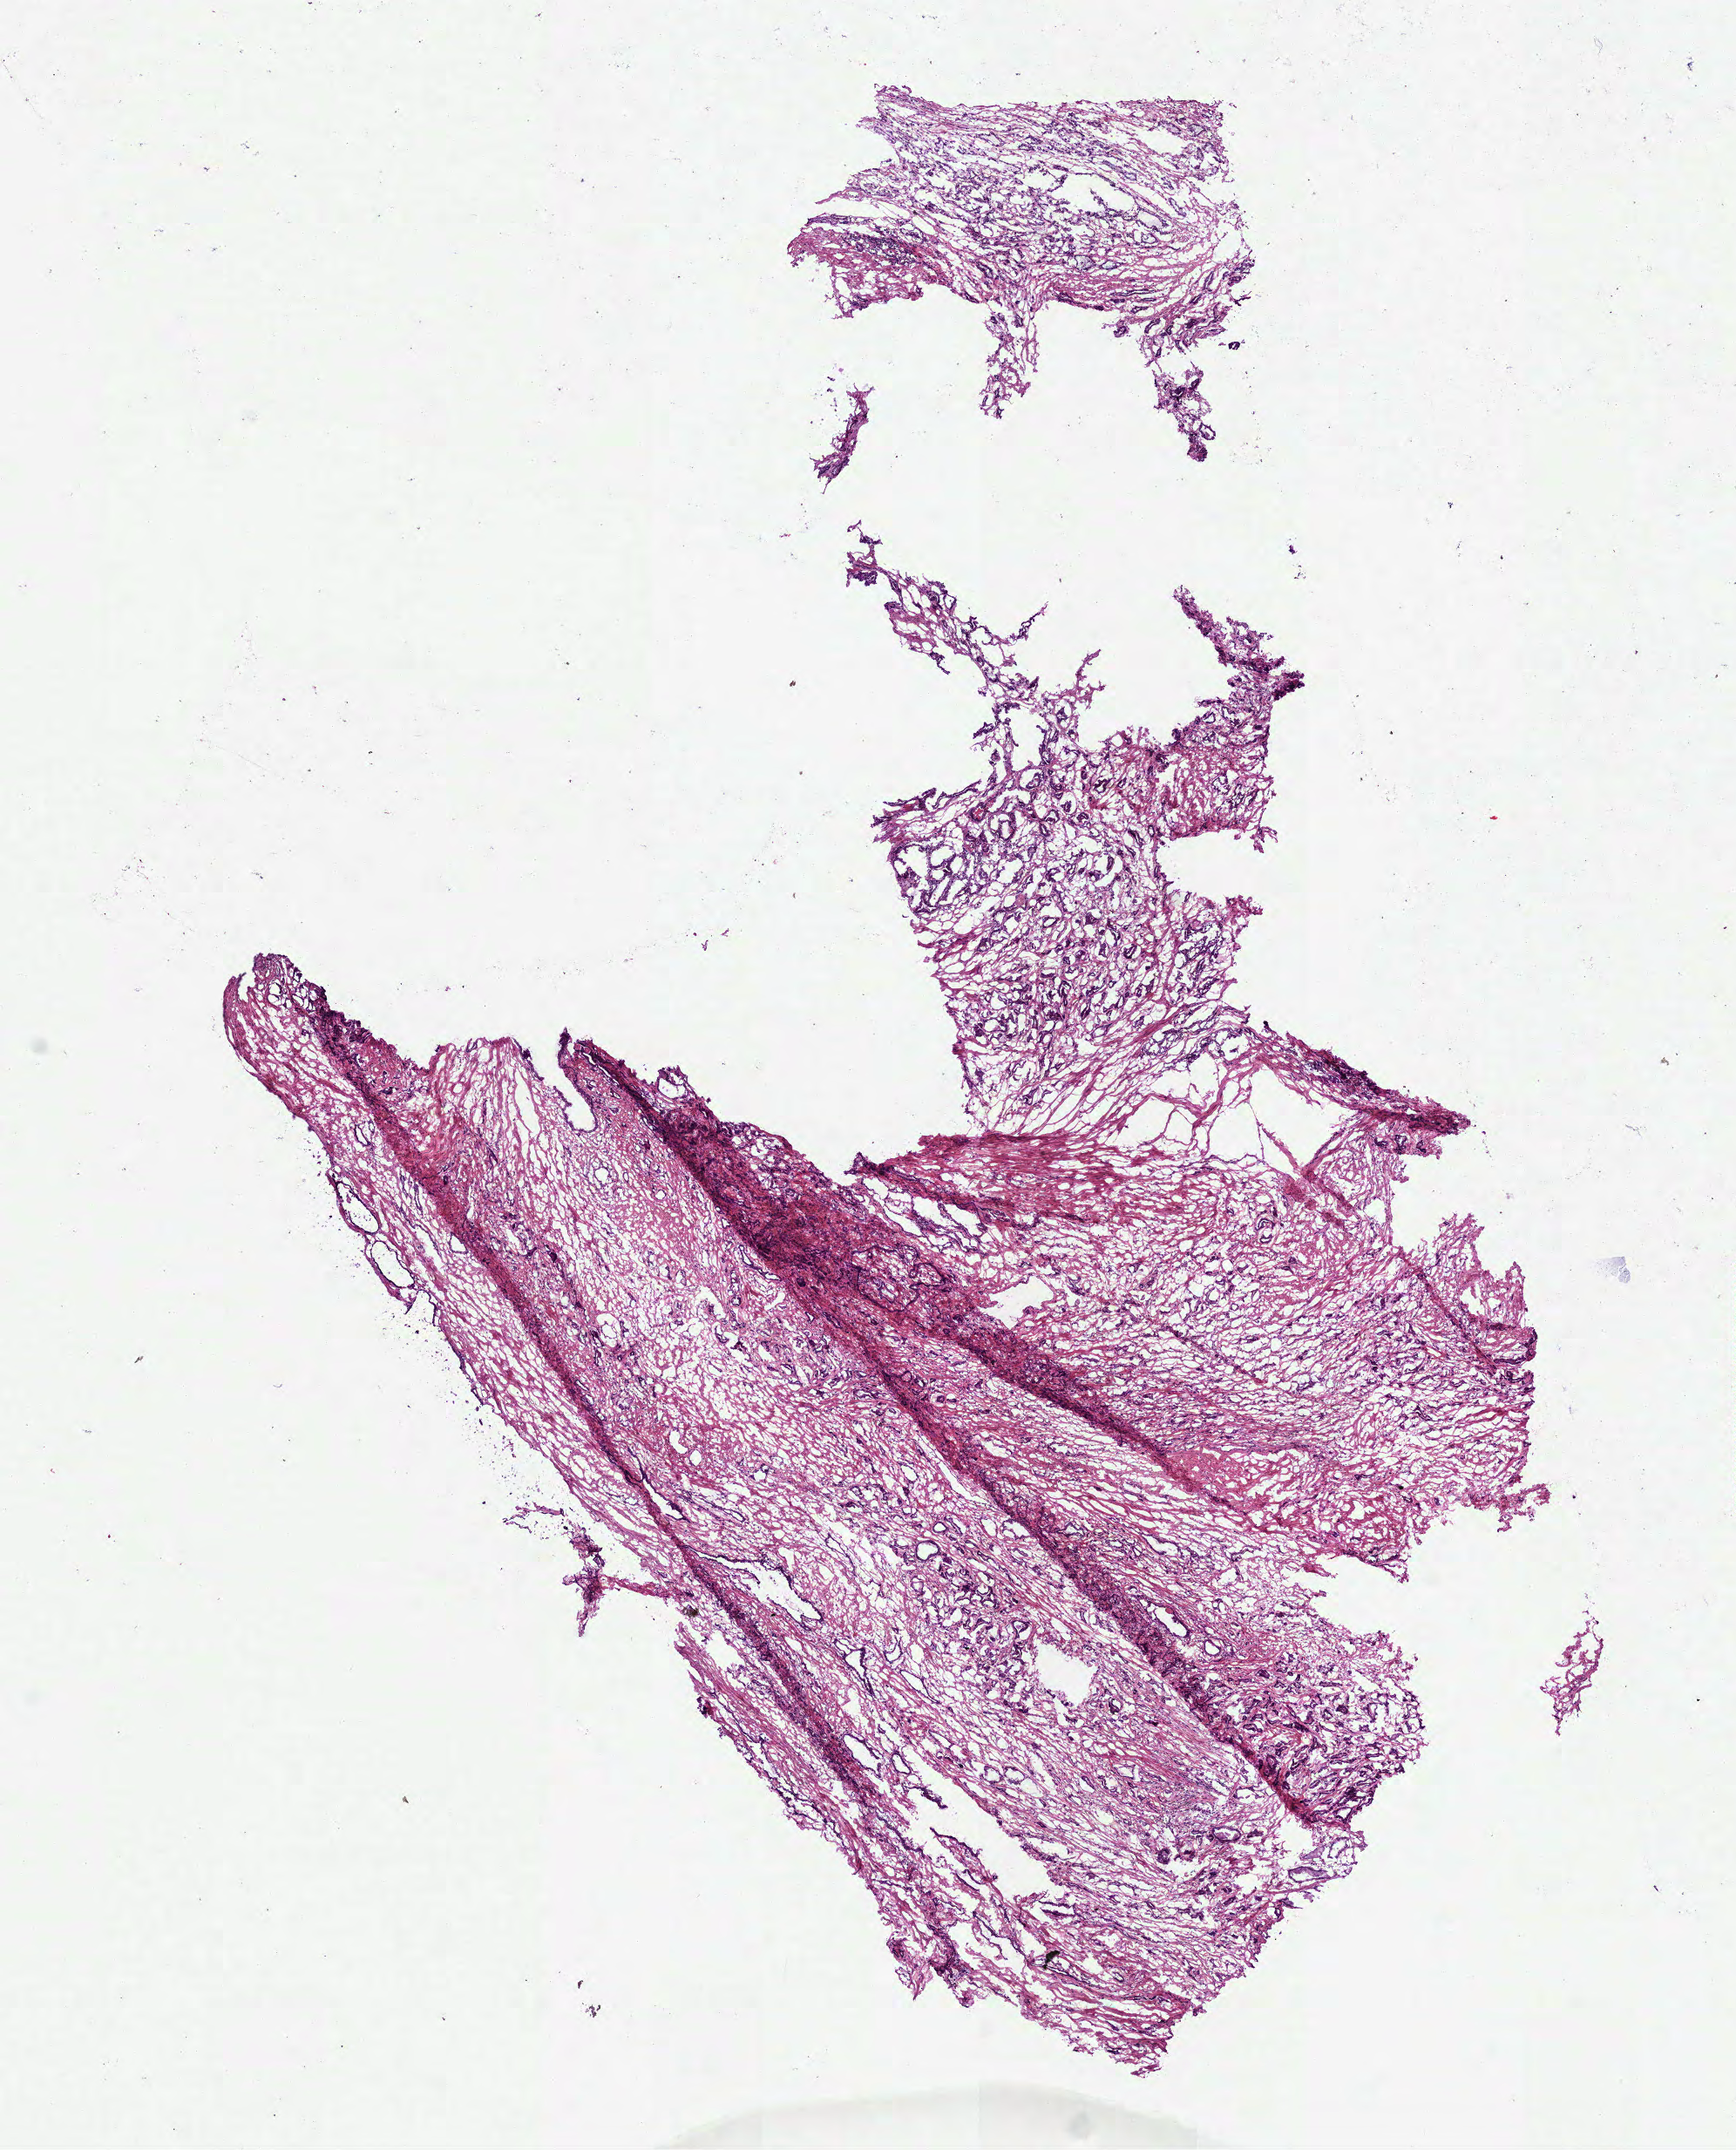
Whole-slide histology image, H&E, shown as a low-resolution overview of the whole scanned area (about 8.0 x 9.9 mm, acquisition: 40x scan), frozen section from the bottom of the tissue portion, primary tumour sample from the prostate. Male patient; age at initial diagnosis 66 years. Gleason score: 7 (4+3). Pathologist review of this section (percent, as recorded): tumour cells 55%, tumour nuclei 55%, normal cells 20%, stromal cells 25%, necrosis 0%. Inflammatory infiltration, as recorded: lymphocyte infiltration 5%, monocyte infiltration 0%, neutrophil infiltration 0%.
- lymph nodes positive (case pathology): 0 of 2 examined
- histologic diagnosis: Acinar cell carcinoma (prostate gland)